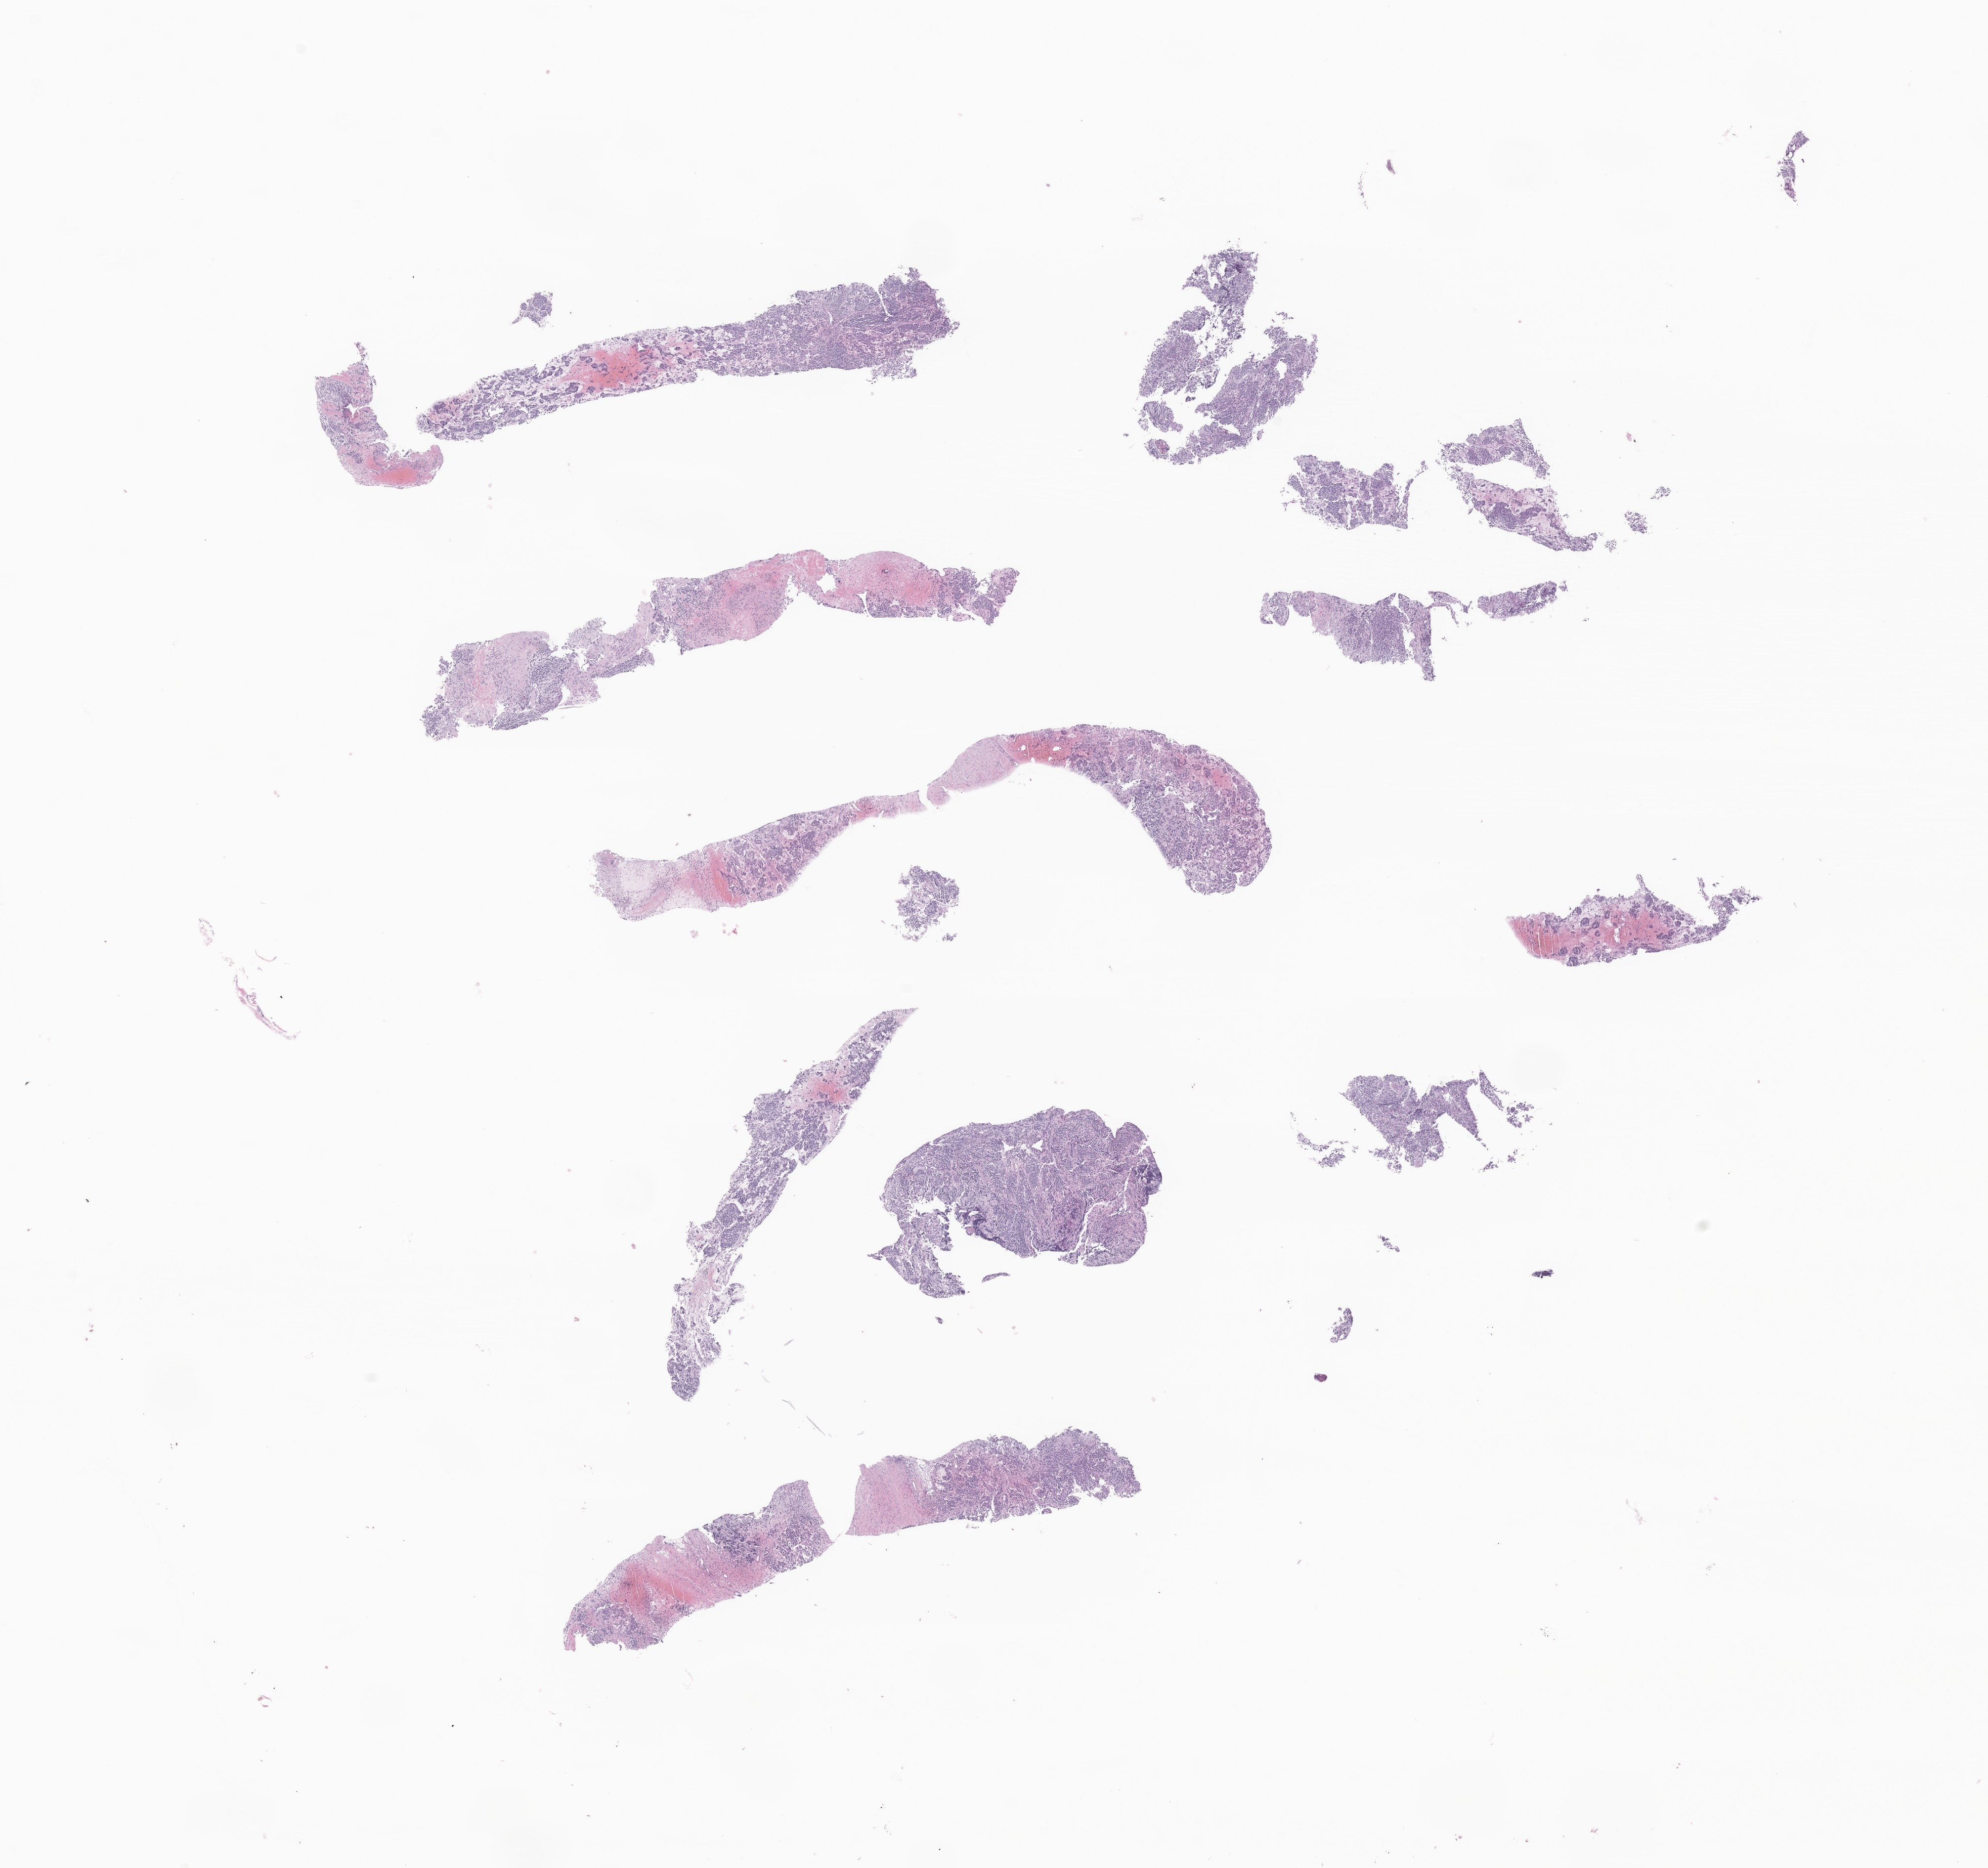
Whole-slide image, hematoxylin and eosin (H&E) stain of tumor tissue from the abdomen, whole scanned area (about 17.0 x 15.9 mm) shown as a low-resolution overview, FFPE section. Patient: female, age 211 days.
Diagnosis (ICD-O-3 morphology term): Neuroblastoma, NOS.